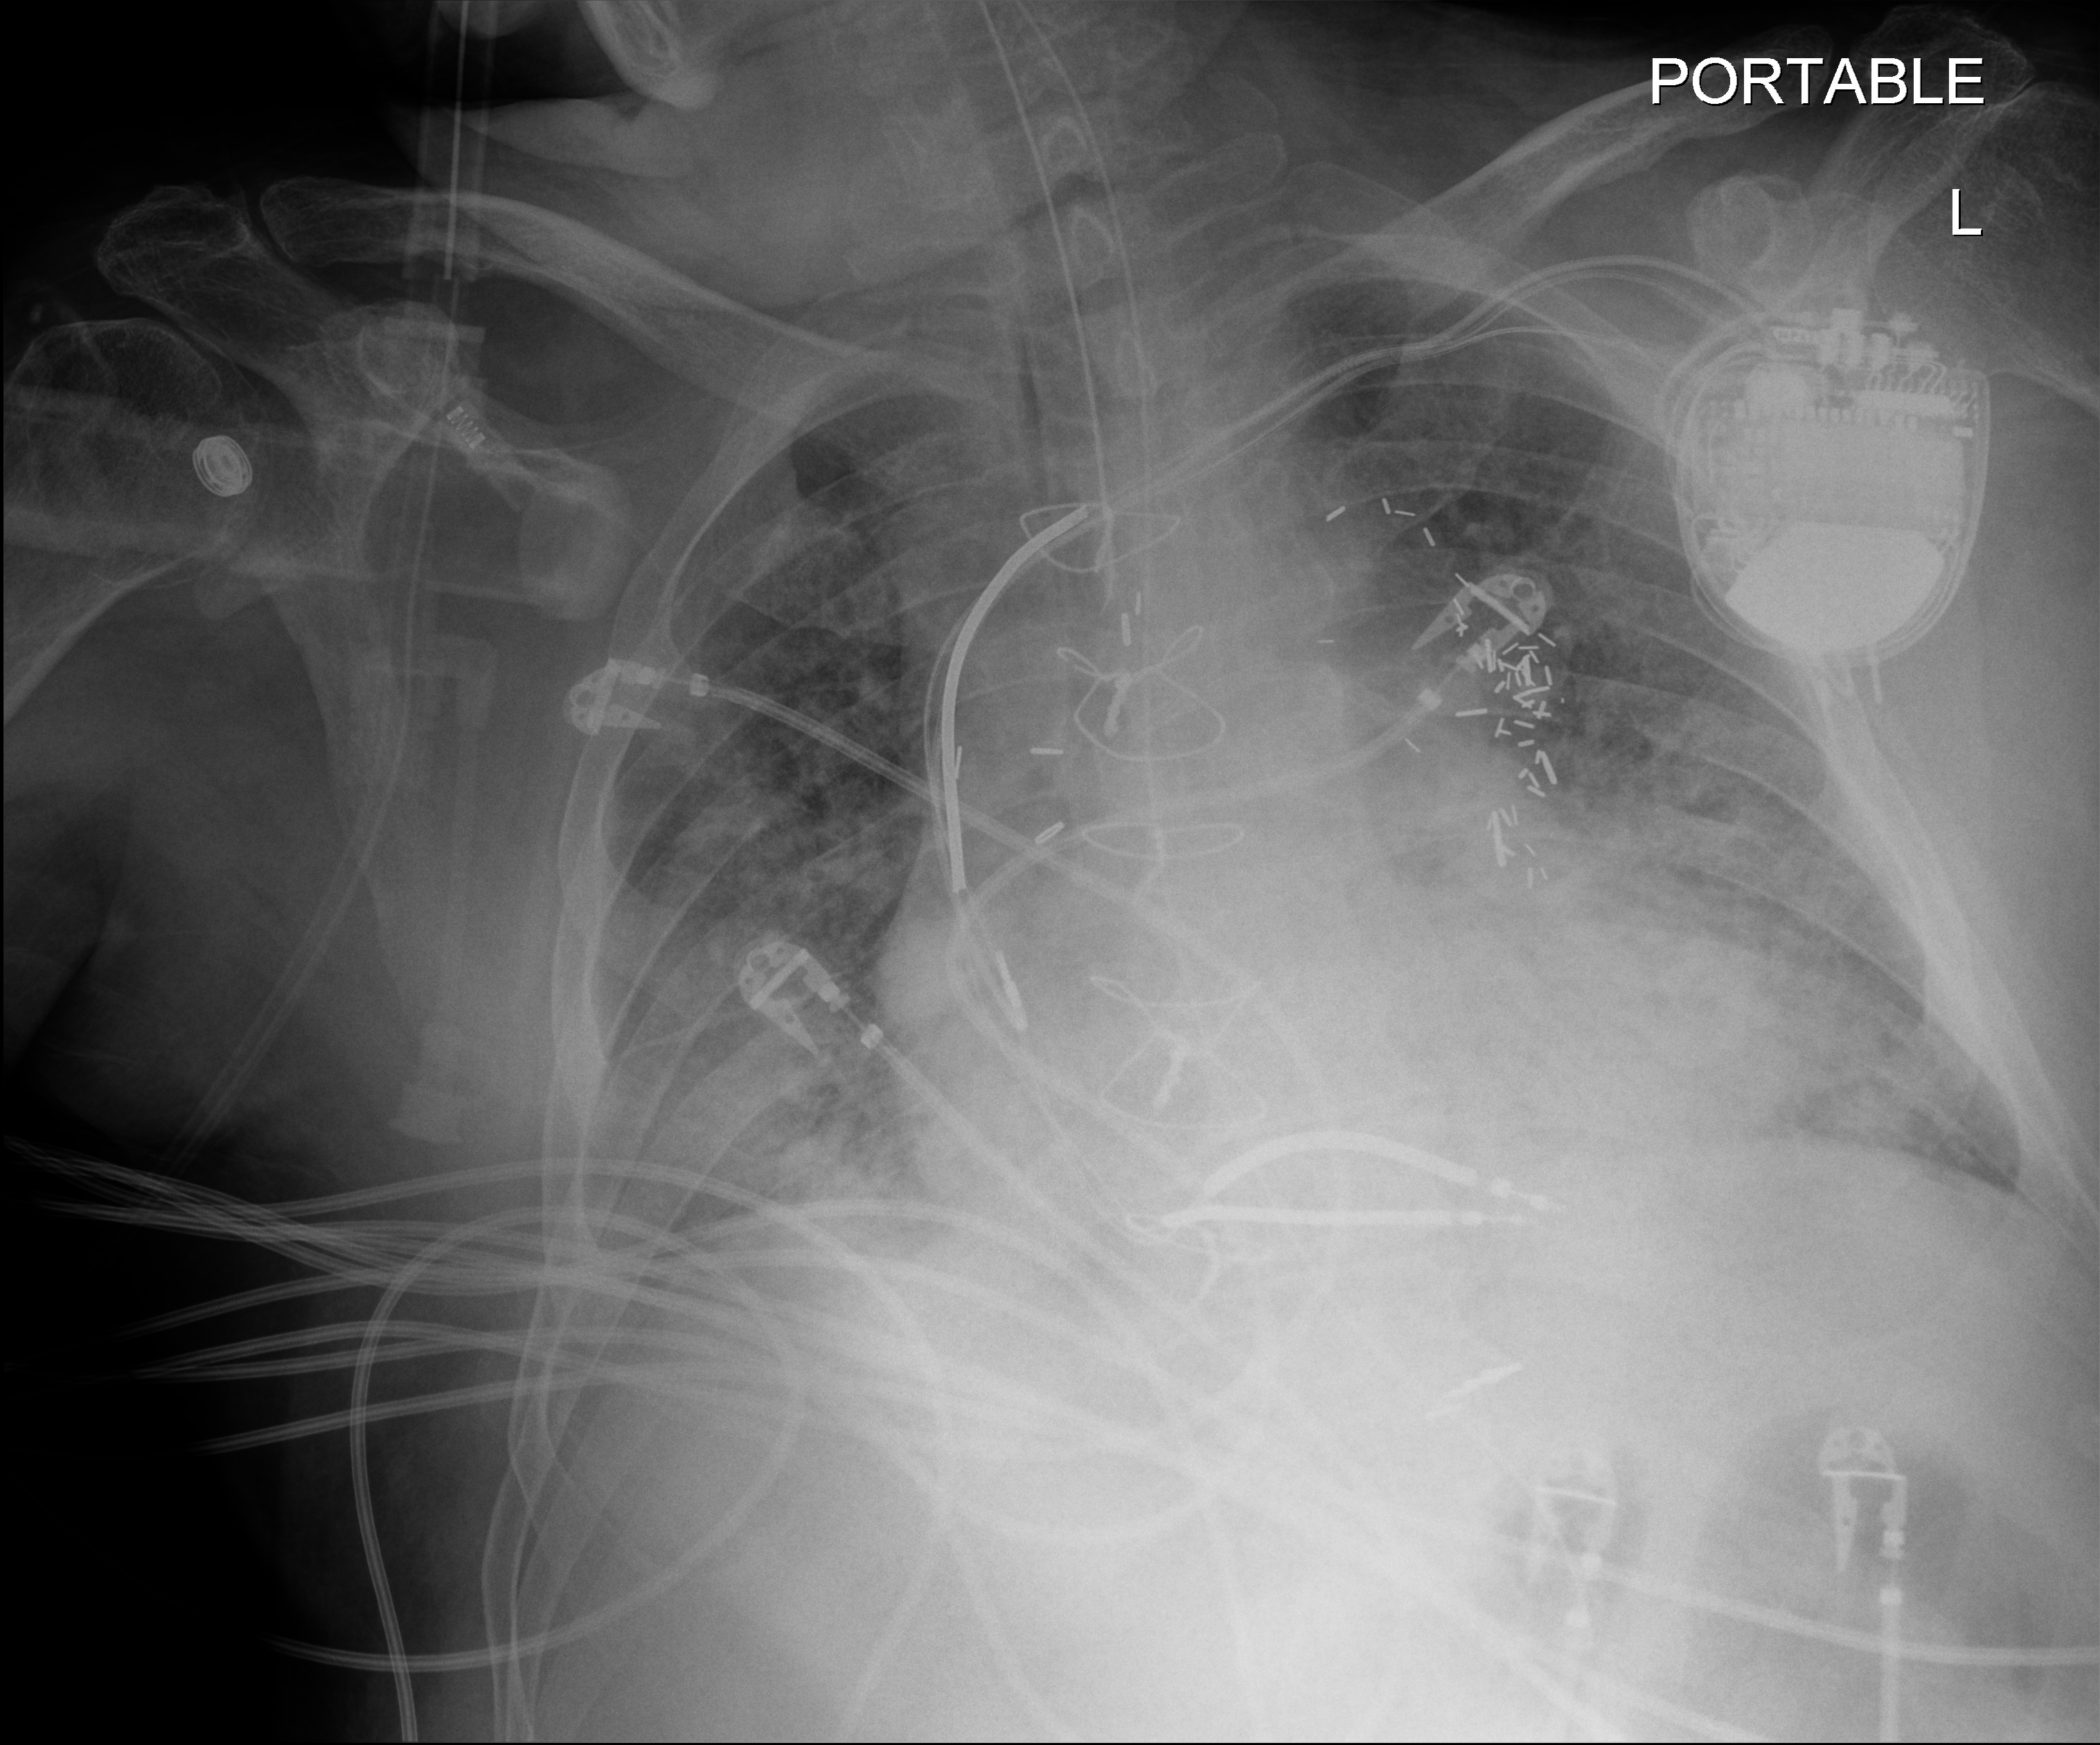
Bedside chest radiograph (digital radiography), anteroposterior (AP) projection. Patient hospitalised with COVID-19; male, aged 60–74 years.
Admission-level facts for this patient (not findings on this image; timing relative to this image not recorded):
- smoking status (admission record): never
- length of hospital stay: 55 days
- admitted to intensive care during this hospital stay: yes